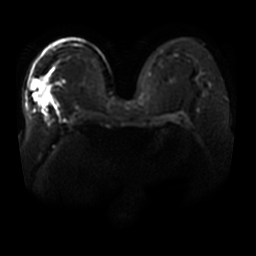
Breast MRI, one axial slice. Slice 26 of 44 in the series (ordered by position). Diffusion-weighted series; image 2 of 4 stored at this slice position (different b-values; order by instance number). 3 T. 5 mm slice thickness. 256 × 256 image matrix. Female patient.
Annotated regions visible in this slice (manually delineated by an expert):
- tumour on diffusion-weighted imaging: bounding box (x1, y1, x2, y2) in pixels: (32, 81, 52, 108)